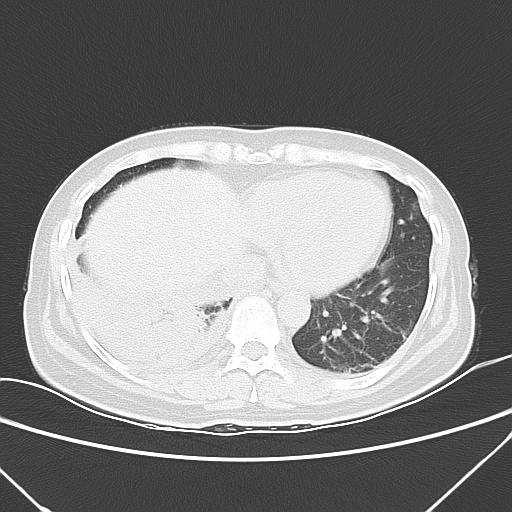
Chest CT, one axial slice. Lung window (W 1500 / L -600 HU). 512 × 512 image matrix, field of view 337 × 337 mm. Patient: female, 42 years. From the clinical record (not read from this slice): clinical TNM (as recorded): T3 N0 M1c.
Structures marked on this image (rectangle marked by the reading radiologist):
- lung tumour (recorded histology: adenocarcinoma): bounding box [x1, y1, x2, y2] px = [78, 277, 214, 371]